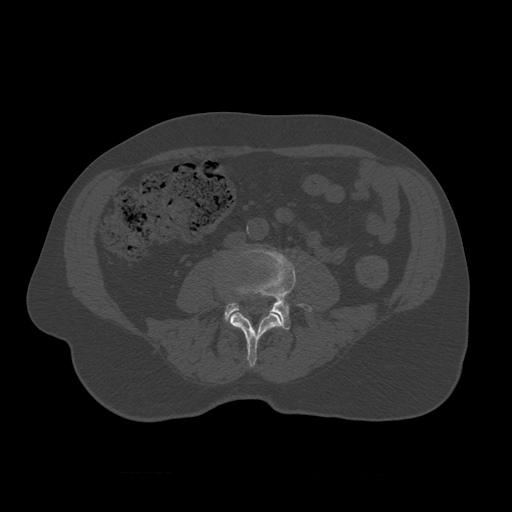
CT including the spine, one axial slice. Slice 289 of 450 in the series (ordered by position). 120 kVp. Bone window (W 1800 / L 400 HU). 512 × 512 image matrix, field of view 405 × 405 mm. Patient age 75 years. Case-level facts recorded for this patient, not image findings: primary cancer: prostate.
Structures marked on this image (semi-automatically segmented with operator editing):
- L3 vertebra: bounding box (x1, y1, x2, y2) in pixels: (230, 296, 283, 368)
- L4 vertebra: (224, 248, 313, 330)